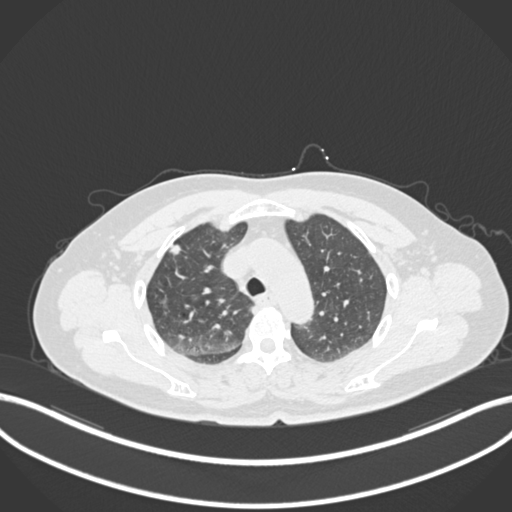
Chest CT, one axial slice. Slice 173 of 223 in the series (ordered by position). 120 kVp. Lung window (W 1500 / L -600 HU). 1 mm slice thickness. 512 × 512 image matrix, field of view 400 × 400 mm. Patient: female, 56 years. From the clinical record (not read from this slice): clinical TNM (as recorded): T1c N0 M0.
Annotated regions visible in this slice (rectangle marked by the reading radiologist):
- lung tumour (recorded histology: adenocarcinoma): box from (x=164, y=240) to (x=190, y=257) px